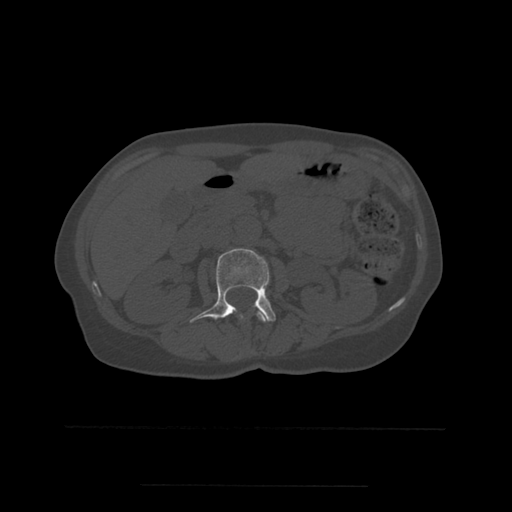
CT including the spine, one axial slice; slice 217 of 544 in the series (ordered by position); bone window (W 1800 / L 400 HU); 1.25 mm slice thickness; 512 × 512 image matrix. Patient age 58 years. Case-level facts recorded for this patient, not image findings: primary cancer: lung.
Annotated regions visible in this slice (semi-automatically segmented with operator editing):
- L1 vertebra: bounding box [x1, y1, x2, y2] px = [257, 310, 267, 322]
- L2 vertebra: [190, 248, 276, 323]